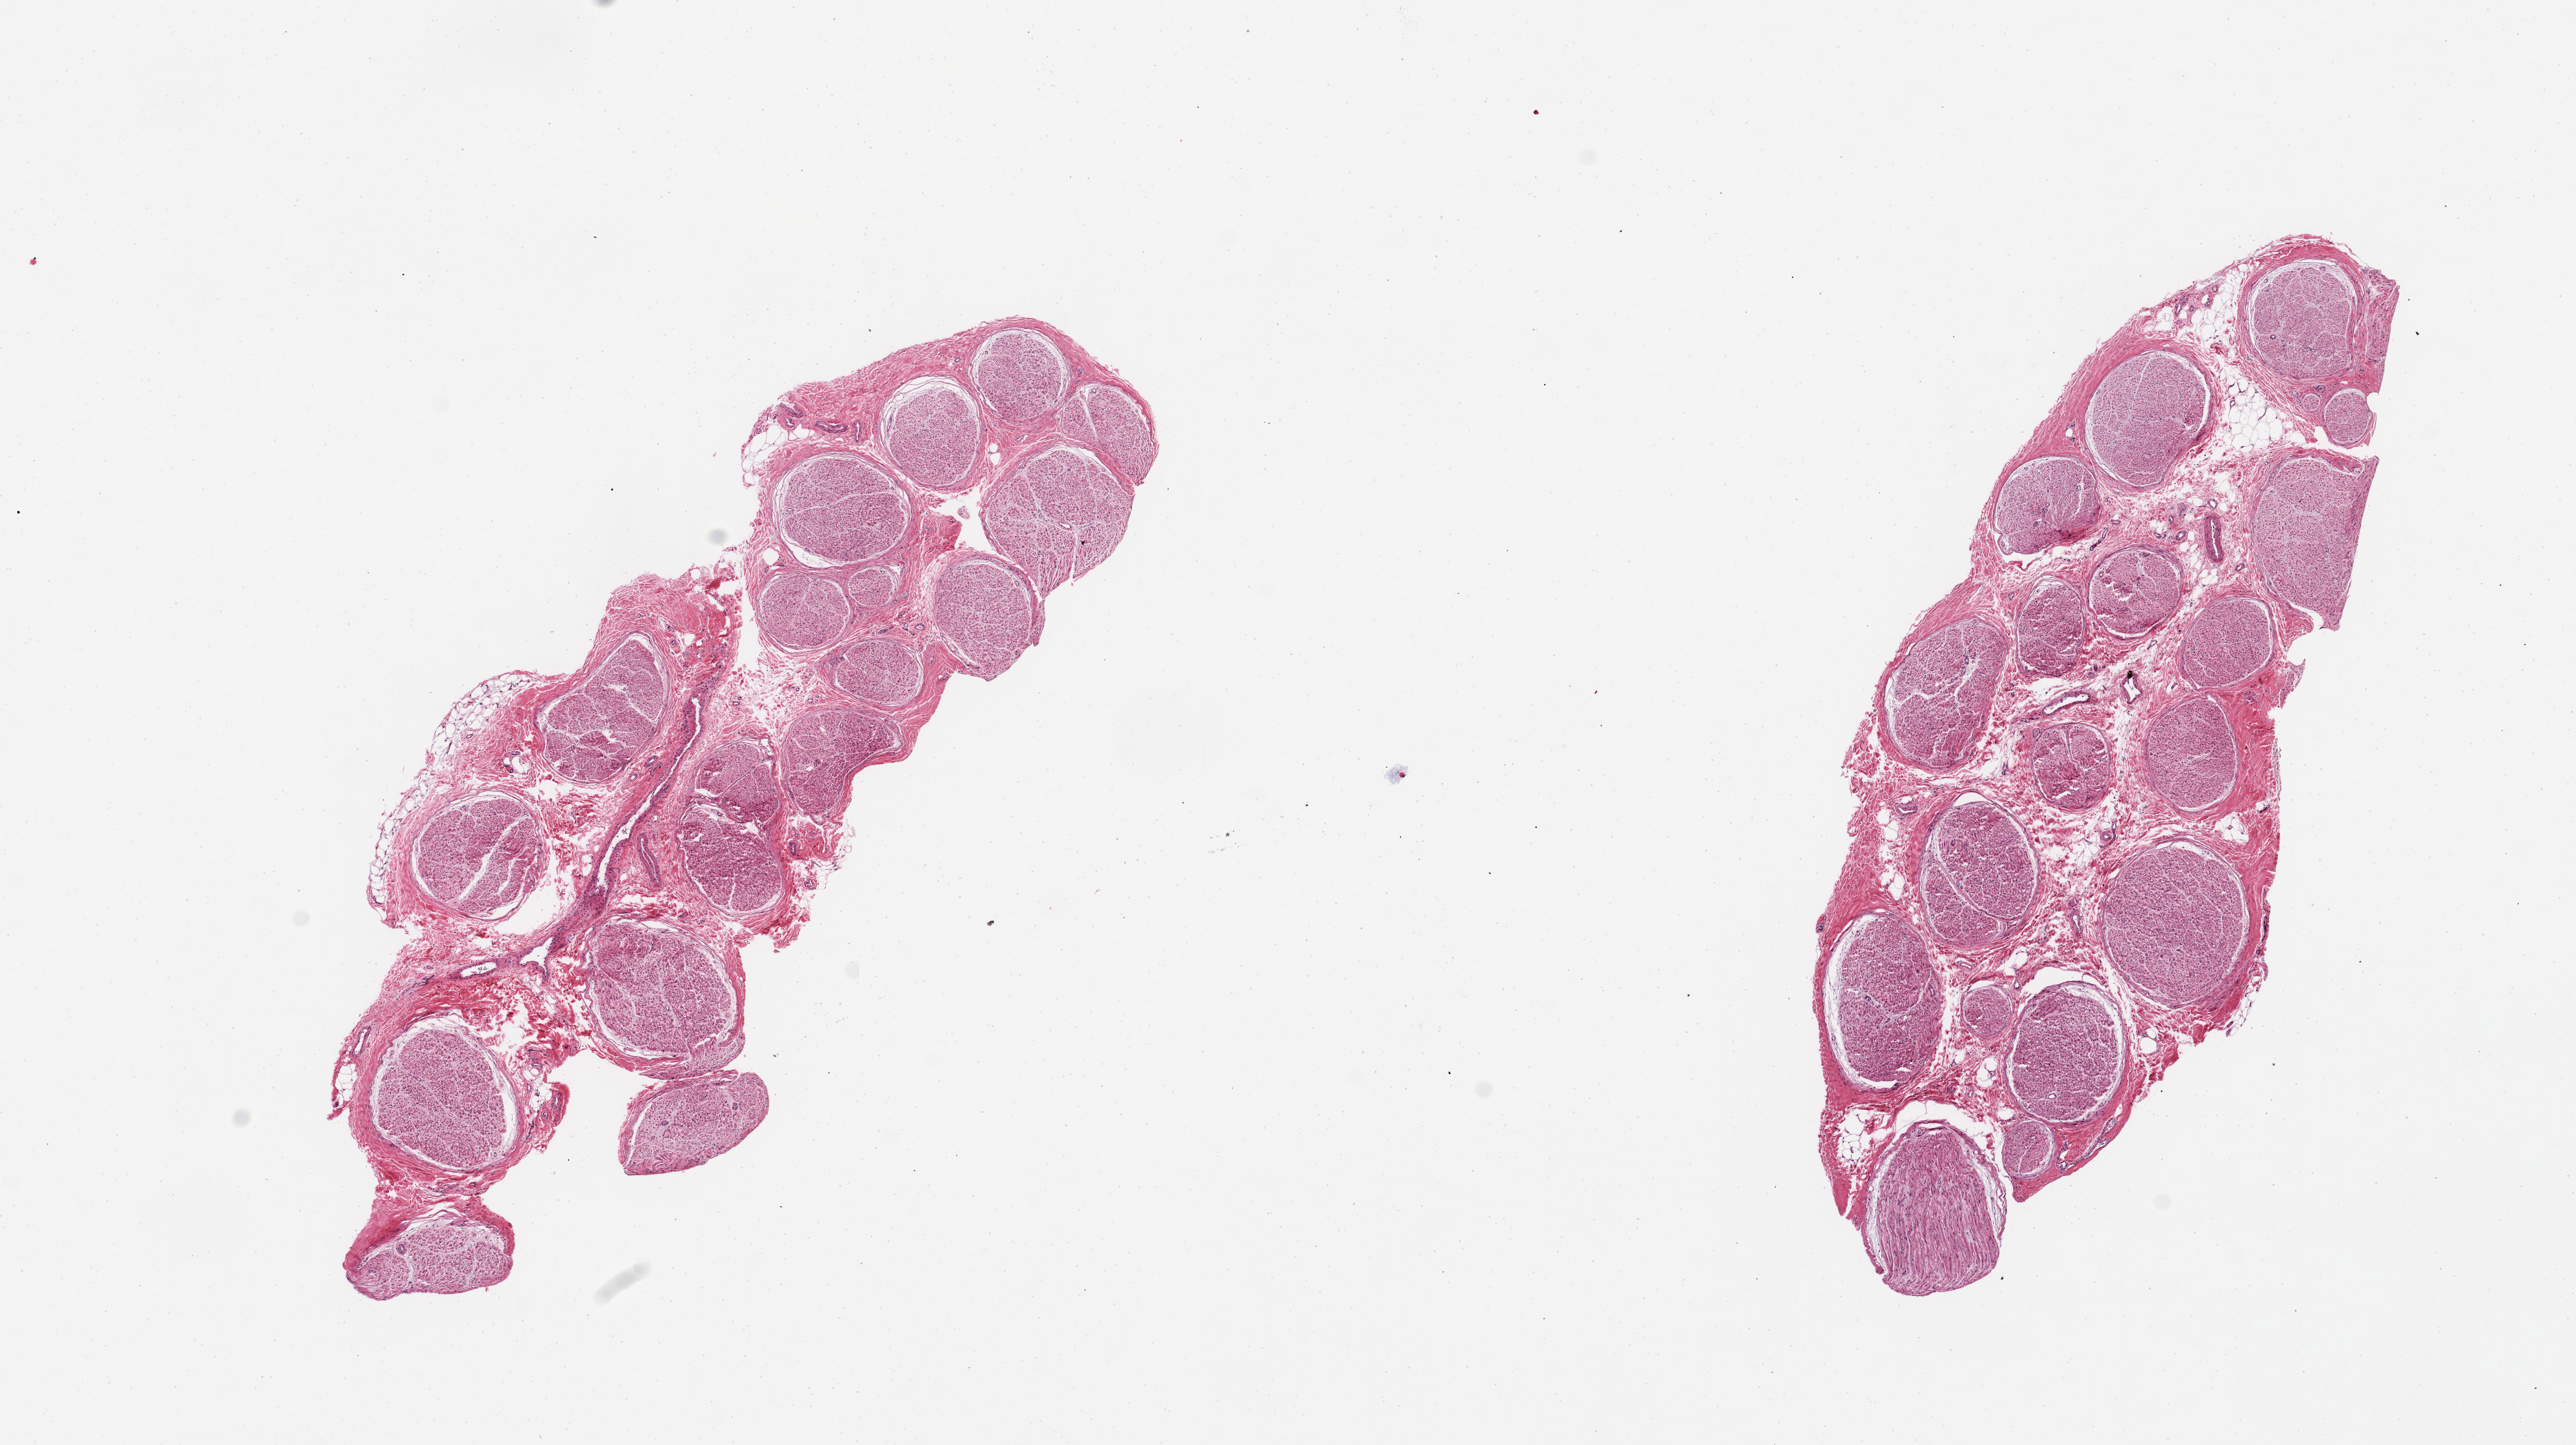
Whole-slide image, hematoxylin and eosin (H&E) stain, brightfield — low-resolution overview of the scanned area, about 14.8 x 8.3 mm, PAXgene-fixed, paraffin-embedded tissue, sampled site (target tissue): tibial nerve, tissue donor sample. Donor: male.
Reviewer comment on this tissue sample: 2 pieces, no adherent fat.